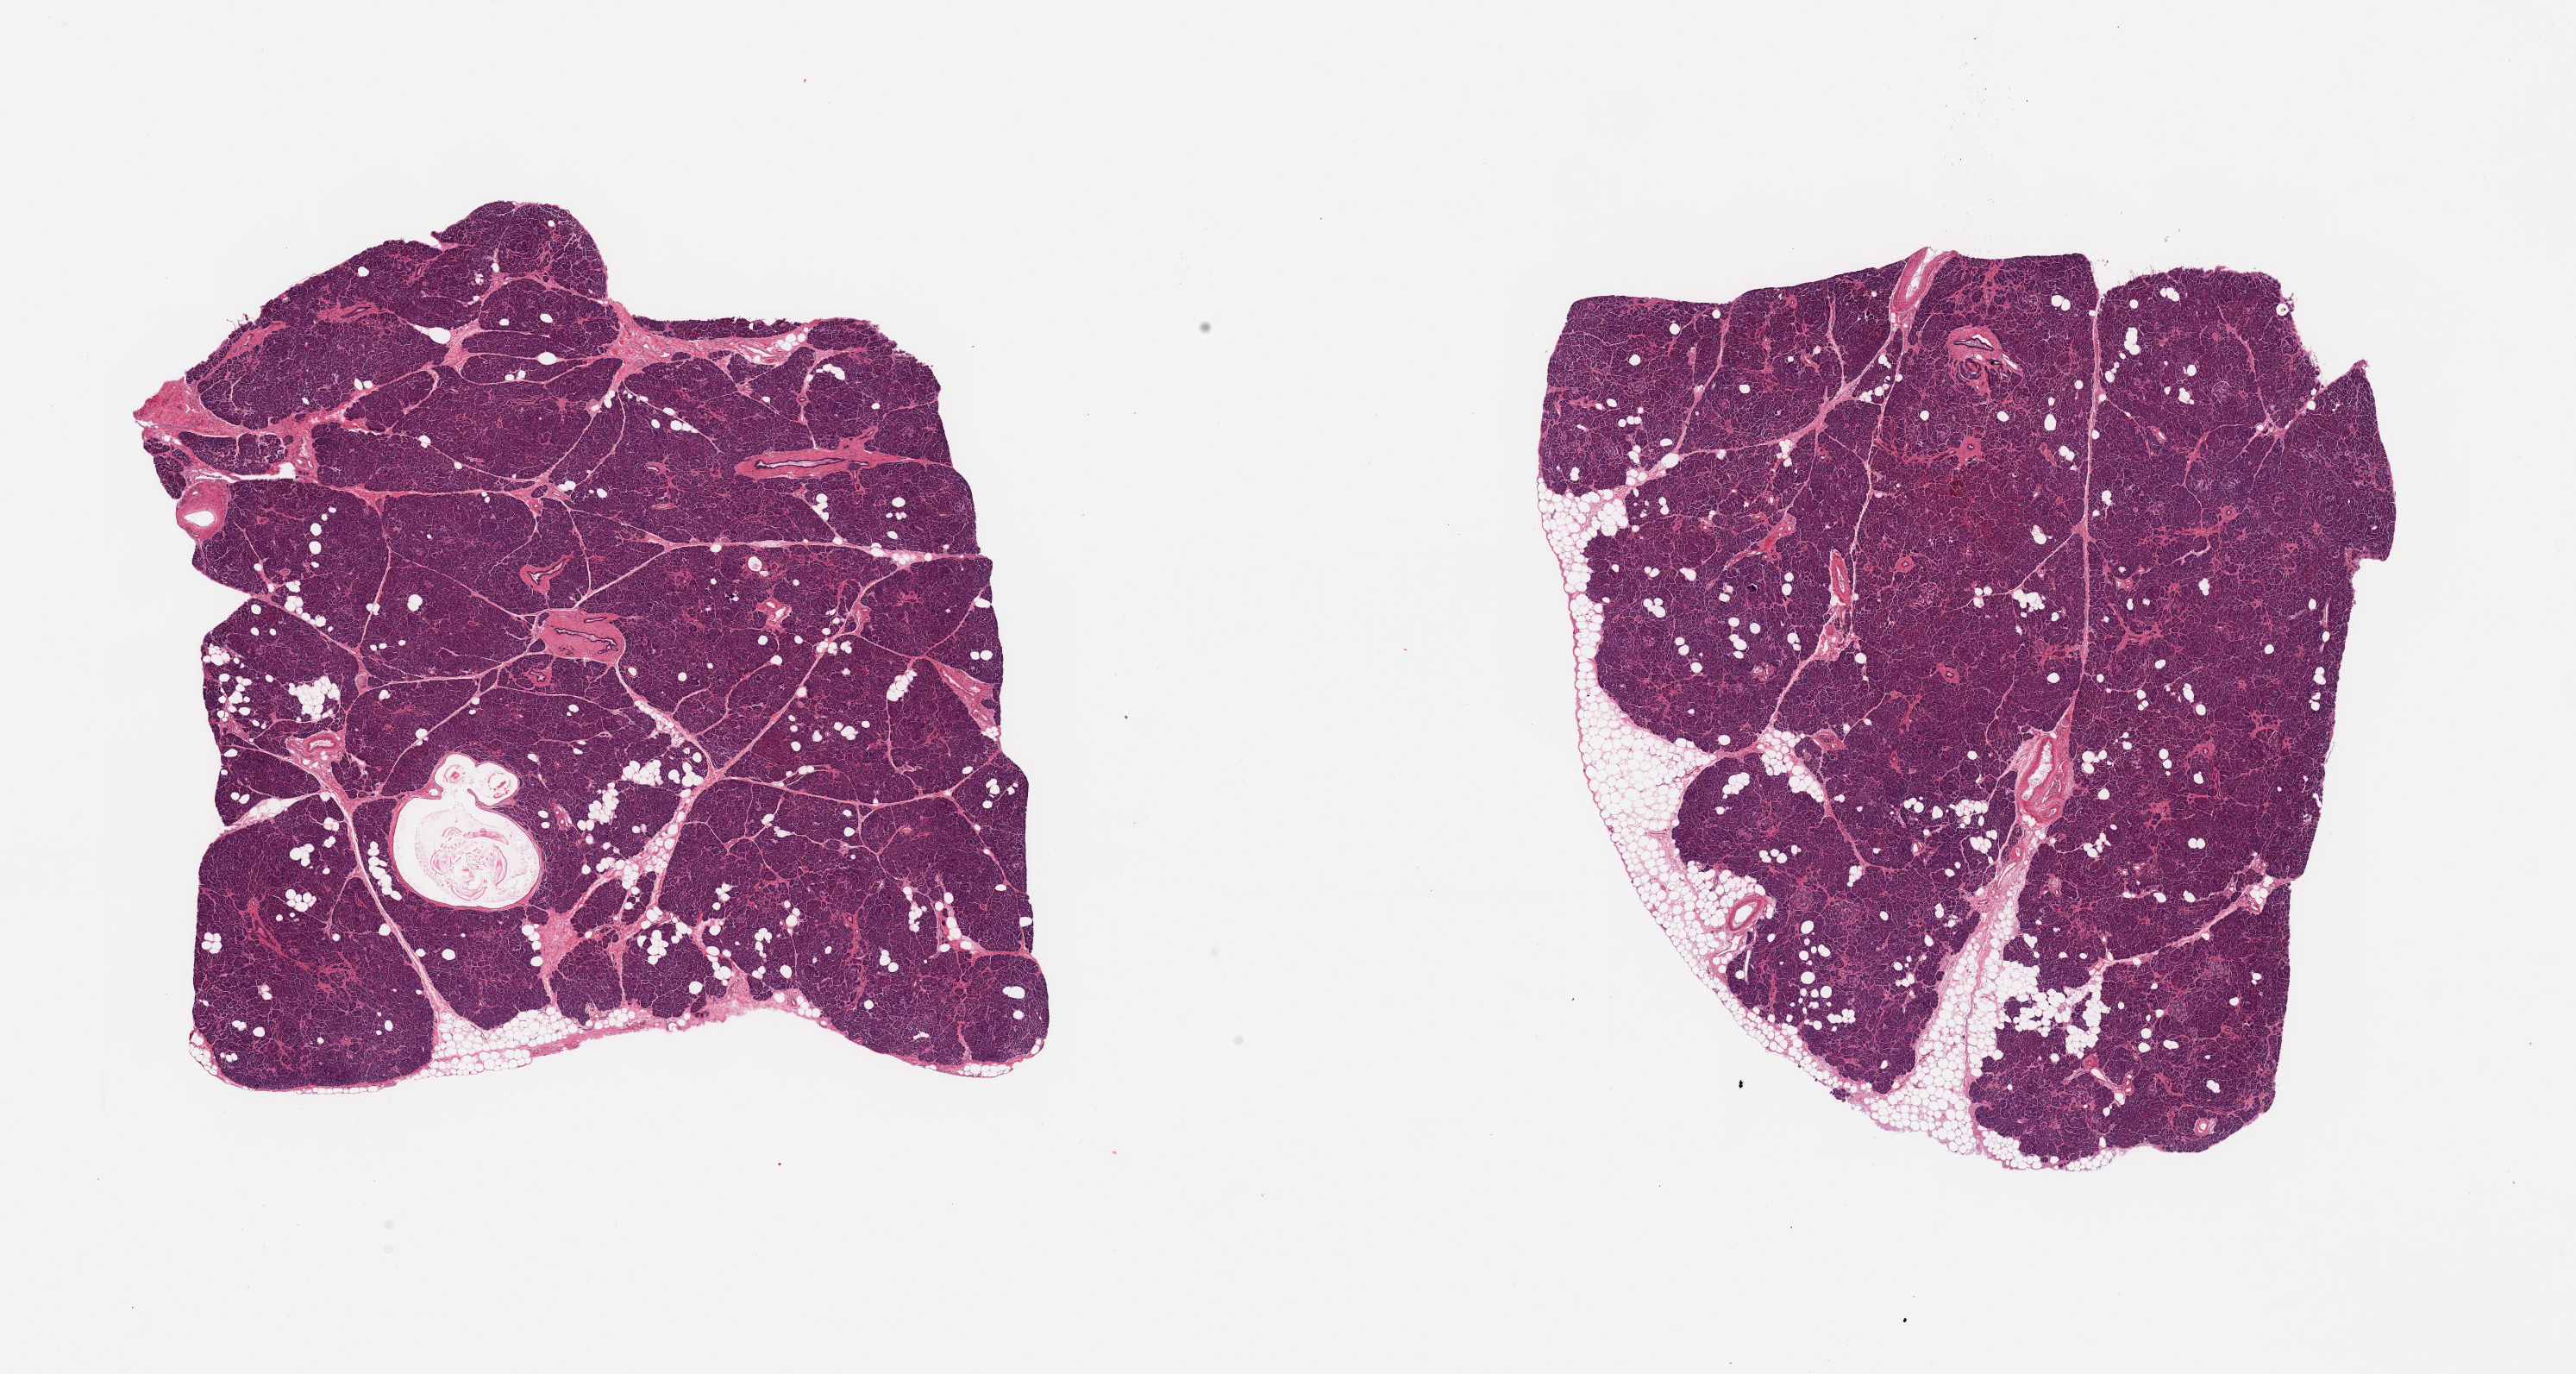
Digitized haematoxylin and eosin-stained section, a low-resolution overview of the entire scanned area, about 23.6 x 12.6 mm (slide scanned at 20x); PAXgene-fixed paraffin-embedded (PFPE) section; section of pancreas (target tissue); donor tissue sample. Donor: male.
Review note (as recorded): 2 pieces, rare but well-preserved Islets.